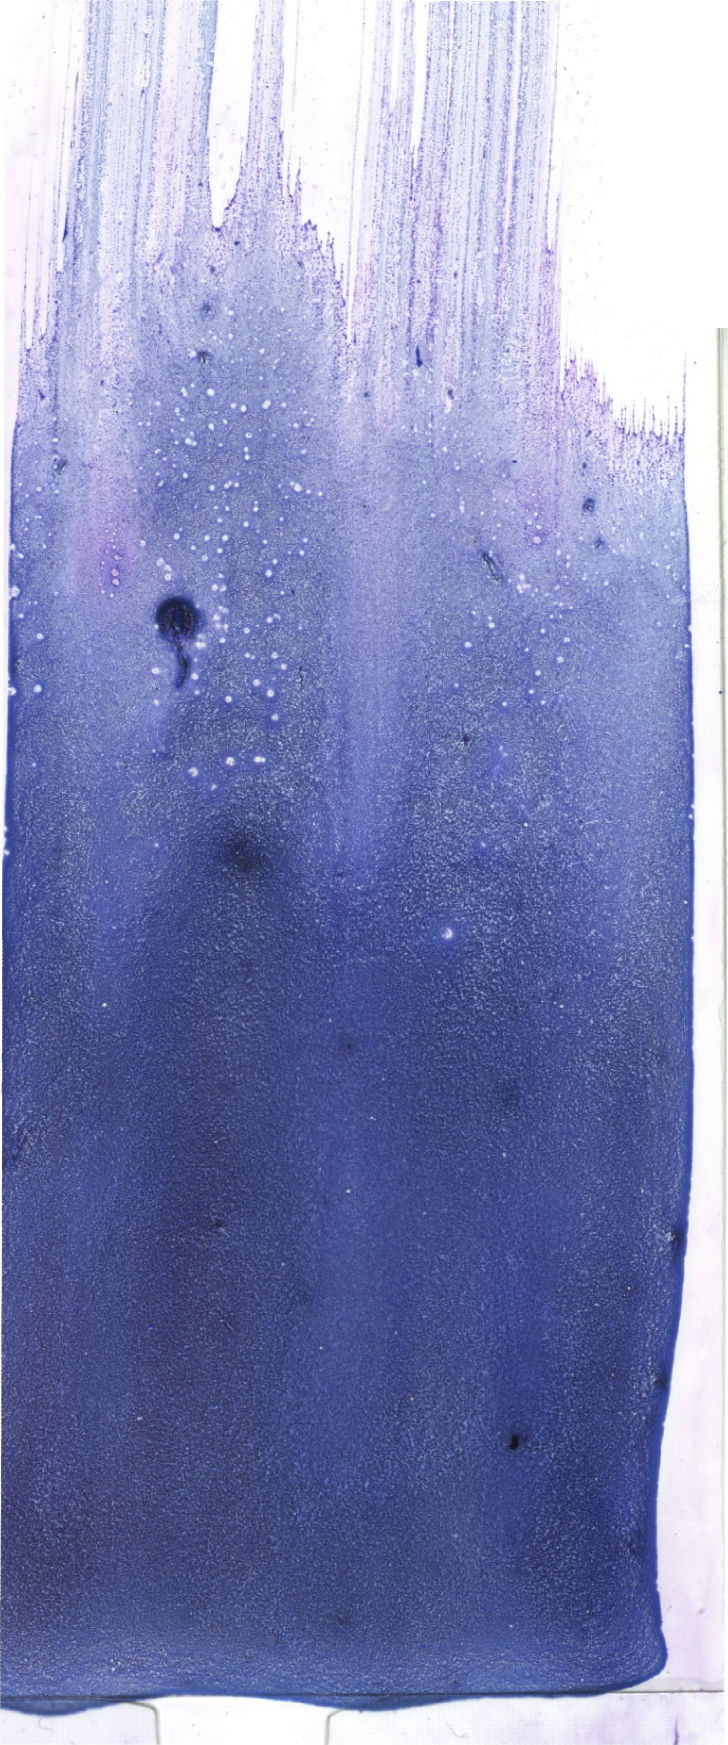
Bone marrow aspirate smear, May-Grünwald-Giemsa (MGG) stain, whole-slide image — low-resolution overview of the scanned area, about 20.6 x 49.5 mm. Patient sex: male.
Diagnosis: Acute Megakaryoblastic Leukemia.